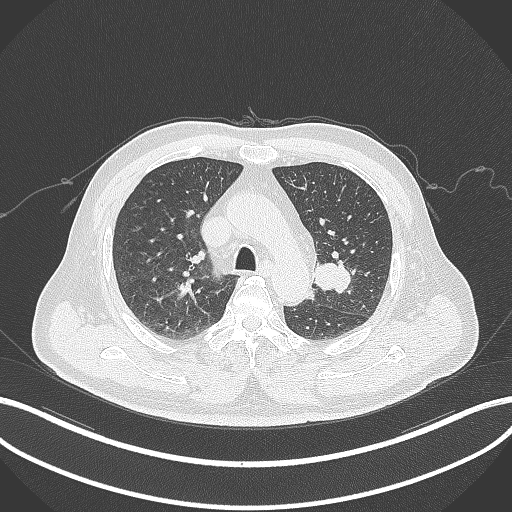
Chest CT, one axial slice; slice 212 of 286 in the series (ordered by position); lung window (W 1500 / L -600 HU); 1 mm slice thickness; 512 × 512 image matrix, field of view 400 × 400 mm. Patient: male, 67 years. From the clinical record (not read from this slice): clinical TNM (as recorded): T2a N1 M0; histopathological grade: G3.
Annotated regions visible in this slice (rectangle marked by the reading radiologist):
- lung tumour (recorded histology: adenocarcinoma): bounding box <313,260,356,296> (left, top, right, bottom; pixels)